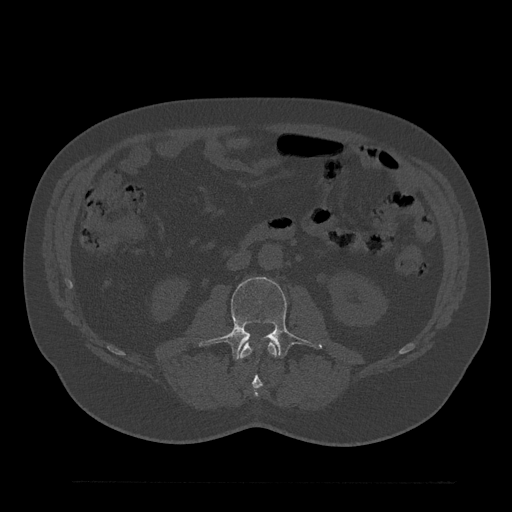
CT including the spine, one axial slice. Slice 52 of 797 in the series (ordered by position). Reconstruction kernel Br40s/3. 120 kVp. Bone window (W 1800 / L 400 HU). 0.5 mm slice thickness. 512 × 512 image matrix, field of view 430 × 430 mm. Male patient, age 61 years. Case-level facts recorded for this patient, not image findings: primary cancer: prostate.
Outlined on this slice (semi-automatically segmented with operator editing):
- L2 vertebra: bounding box (x1, y1, x2, y2) in pixels: (239, 342, 278, 397)
- L3 vertebra: (199, 277, 322, 360)